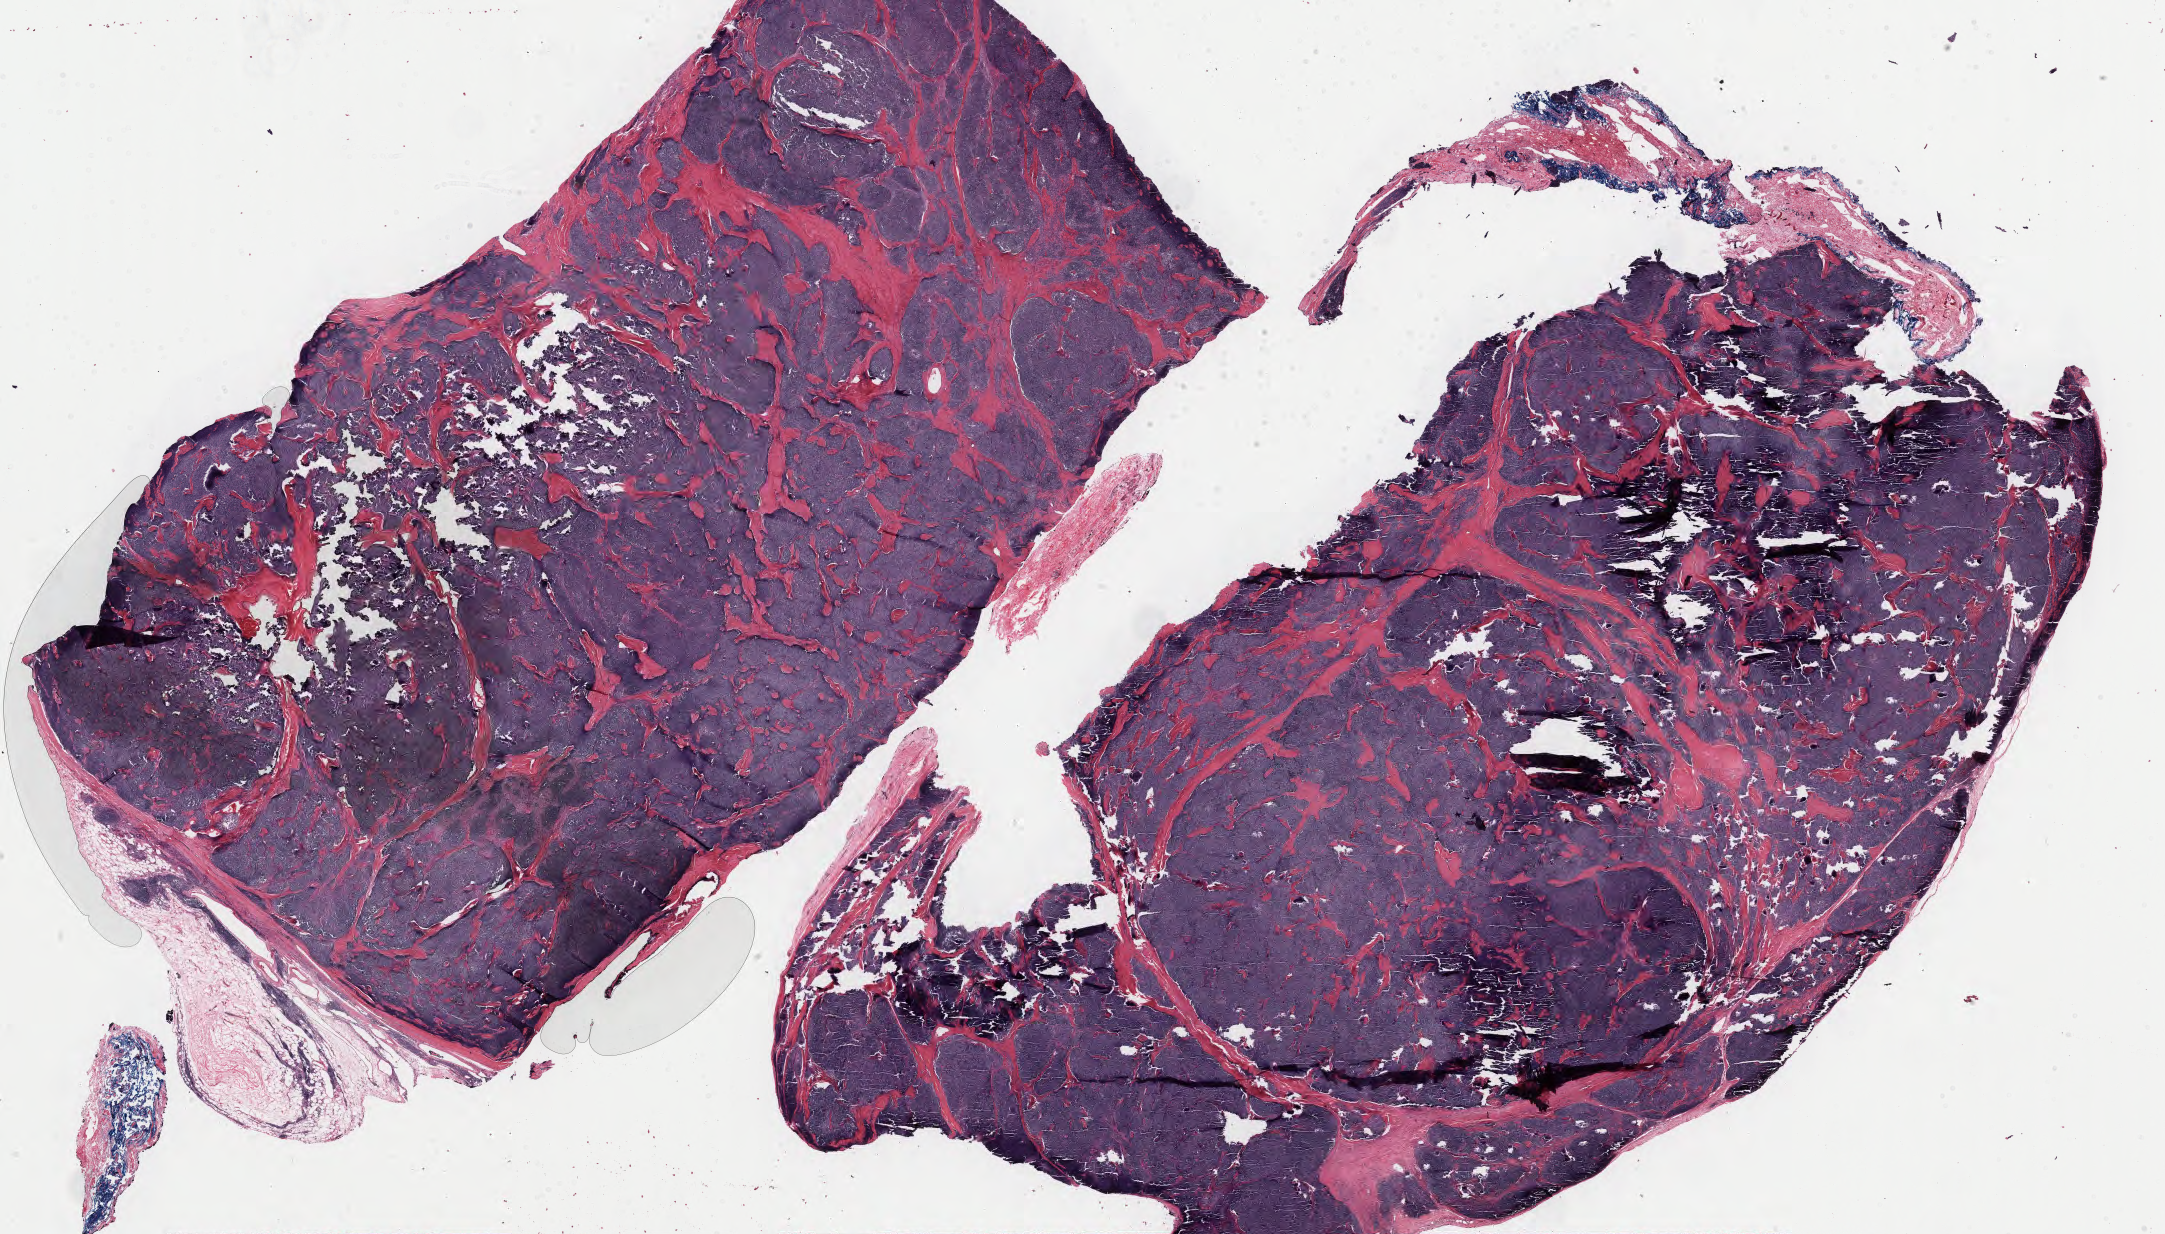
H&E whole-slide image — shown as a low-resolution overview of the whole scanned area (about 34.3 x 19.6 mm, acquisition: 40x scan). Formalin-fixed paraffin-embedded (FFPE) diagnostic section. Sample: primary tumour, thymus. Female patient; age at initial diagnosis 50 years.
Pathologic diagnosis: Thymoma, type AB, malignant.